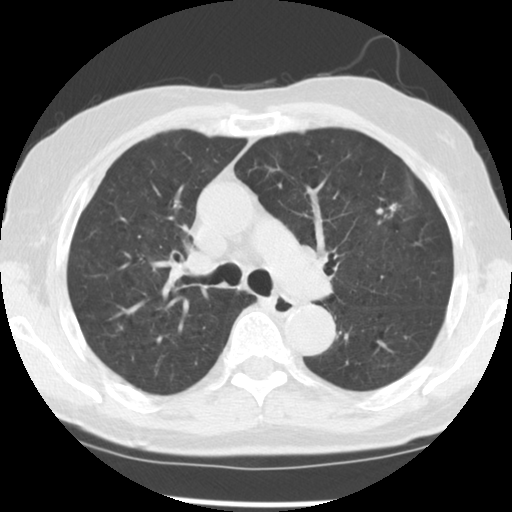
Low-dose screening chest CT, one axial slice. Position 83 of 131 along the scan axis. 140 kVp. Lung window (W 1500 / L -600 HU). 512 × 512 image matrix.
Structures marked on this image (outlined manually by an expert reader):
- lesion 1 (tumor, upper lobe of left lung): bounding box <376,203,397,218> (left, top, right, bottom; pixels)